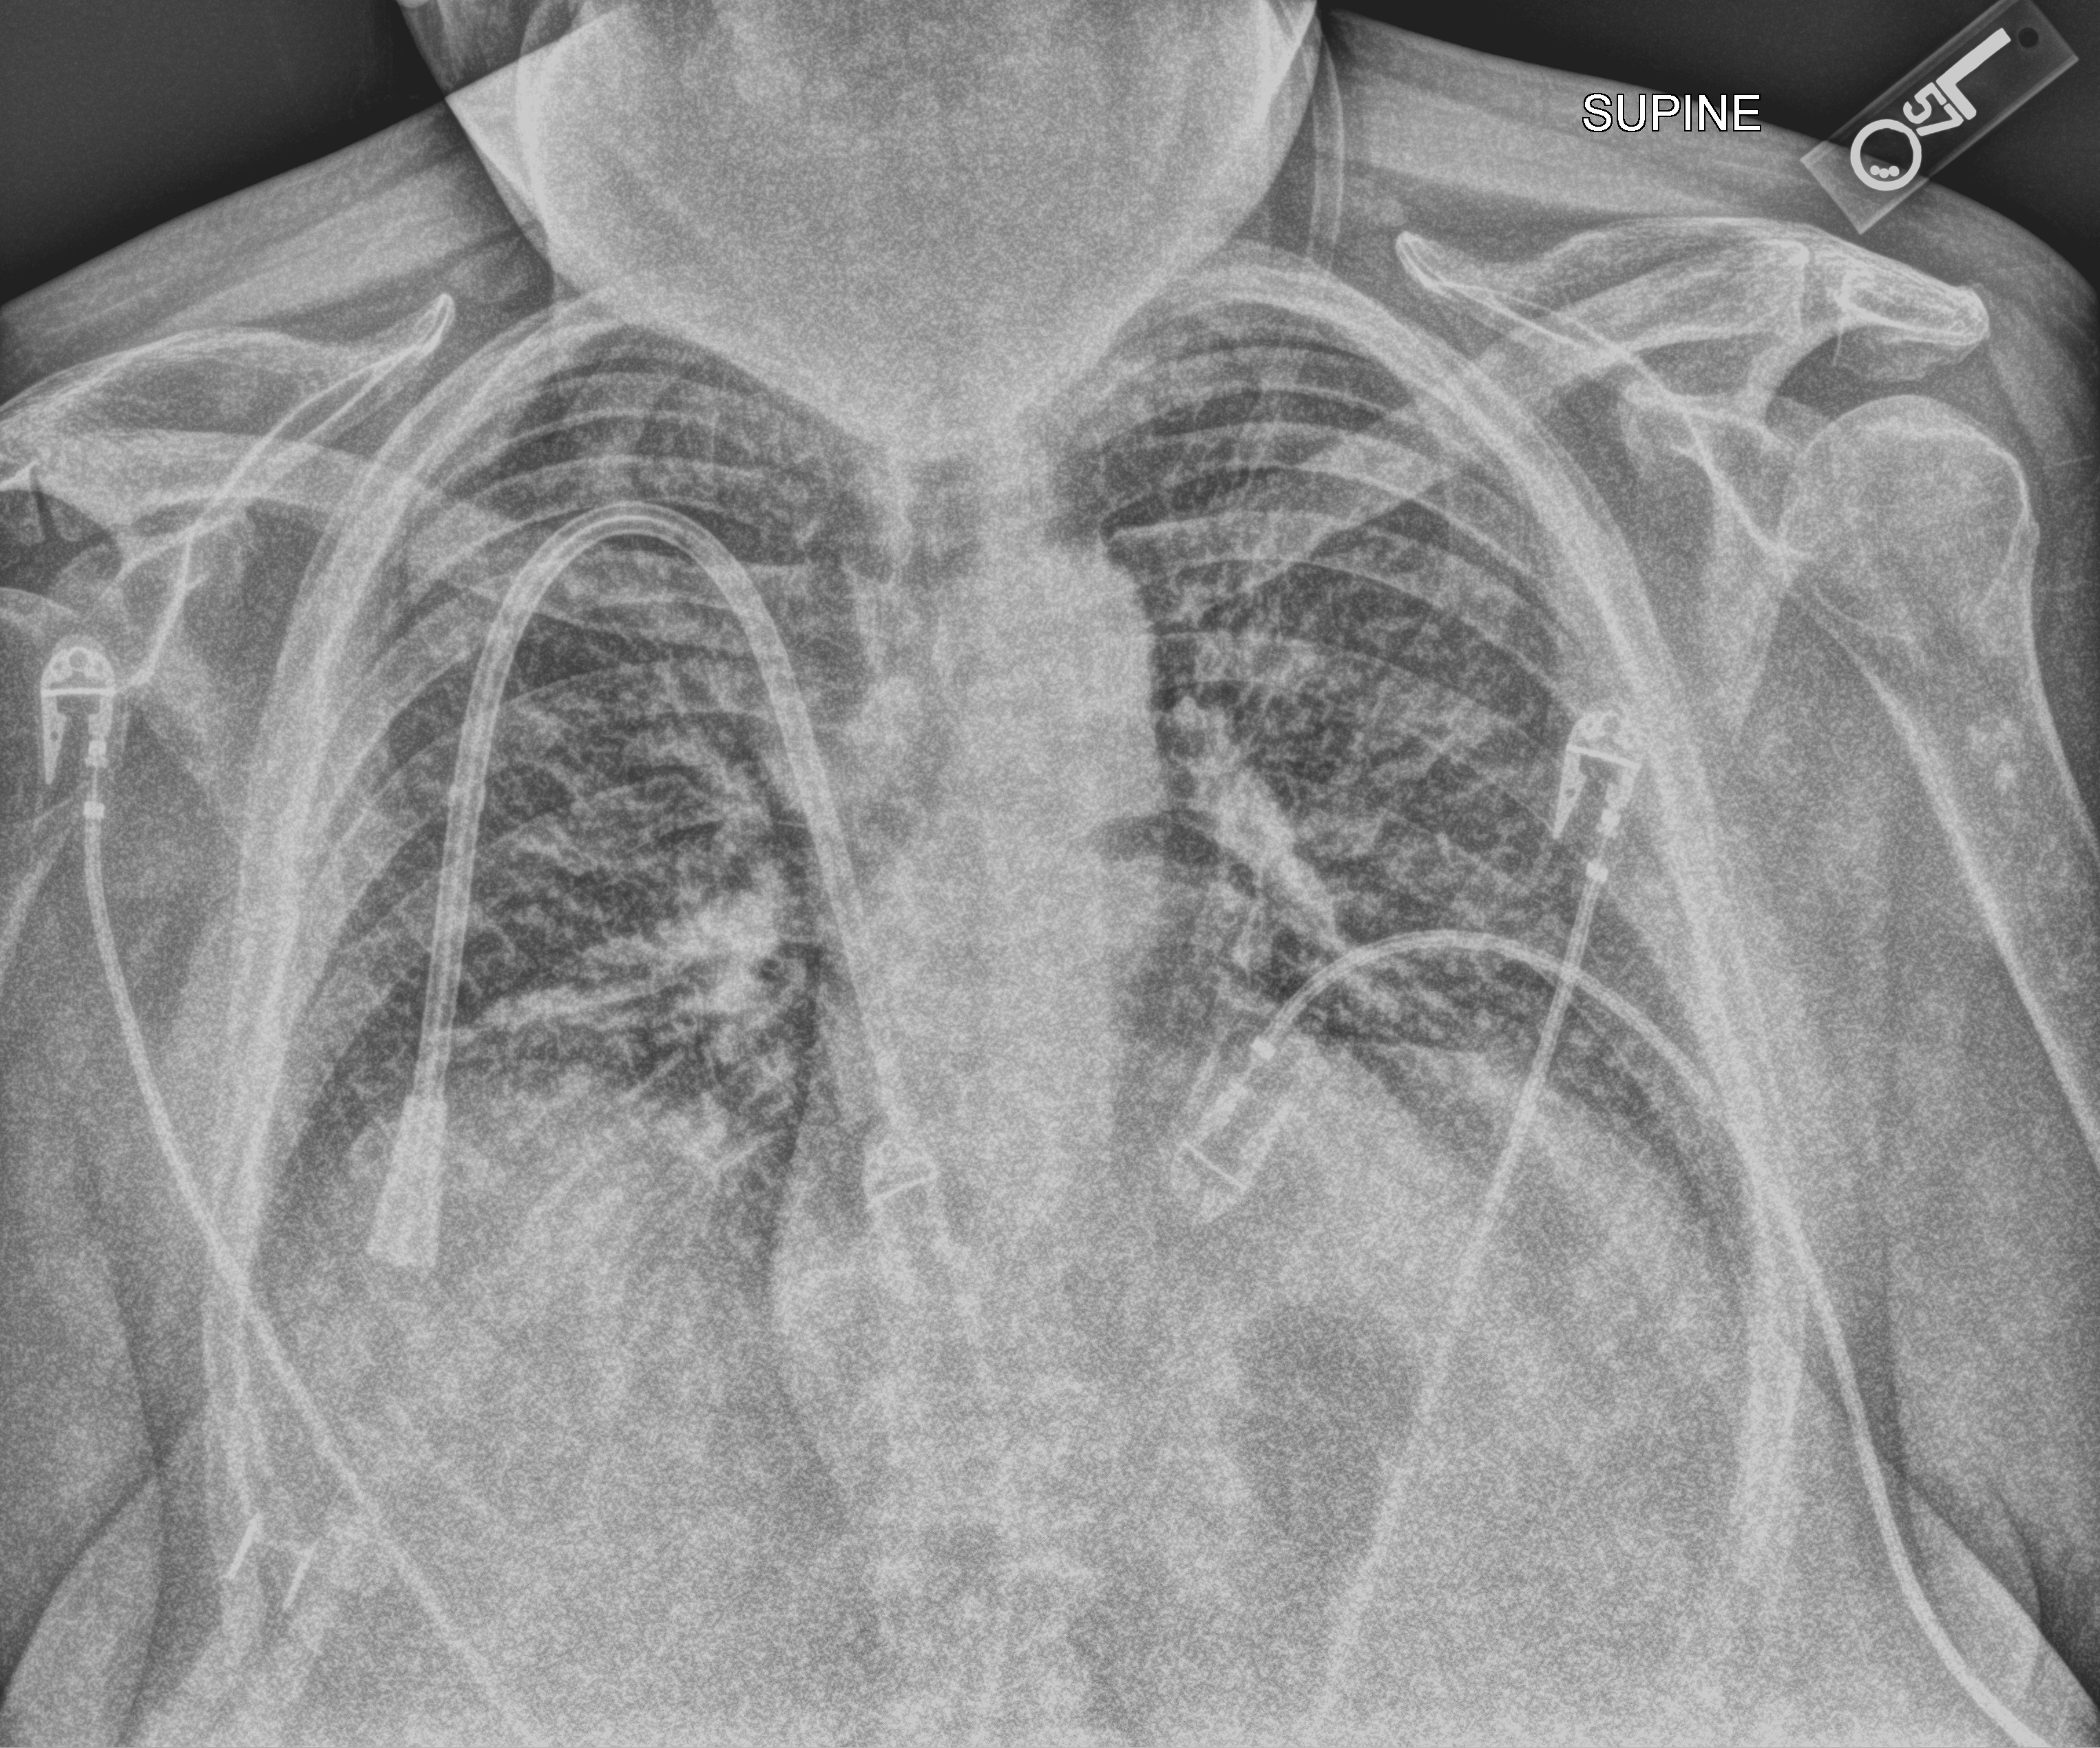
Portable chest radiograph. Patient hospitalised with COVID-19; female, aged 60–74 years.
Hospital-stay facts (about this admission, not read from this image; timing relative to this image not recorded):
- mechanically ventilated during this hospital stay: no